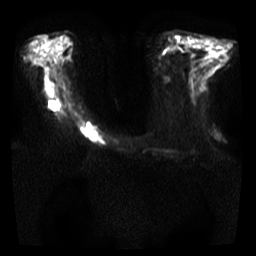
Breast MRI, one axial slice; slice 13 of 35 in the series (ordered by position); diffusion-weighted series; image 2 of 4 stored at this slice position (different b-values; order by instance number); 3 T; 256 × 256 image matrix, field of view 300 × 300 mm. Female patient.
Structures marked on this image (manually delineated by an expert):
- tumour on diffusion-weighted imaging: box from (x=80, y=121) to (x=107, y=145) px